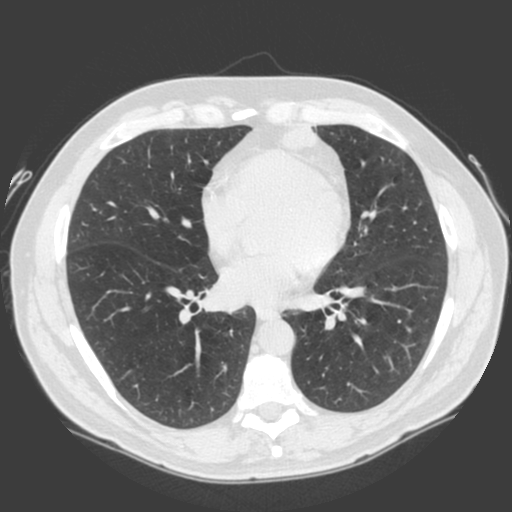
Low-dose screening chest CT, one axial slice; position 85 of 185 along the scan axis; 120 kVp; lung window (W 1500 / L -600 HU); 2 mm slice thickness; 512 × 512 image matrix.
Outlined on this slice (expert manual segmentation):
- lesion 1 (tumor, lower lobe of left lung): bounding box <279,124,339,174> (left, top, right, bottom; pixels)